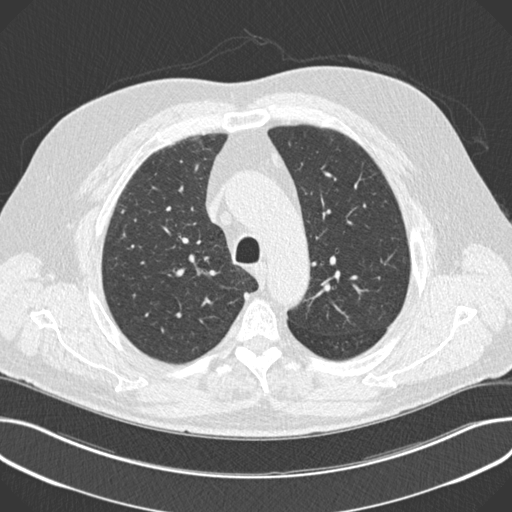
Axial slice from a low-dose chest CT screening exam; first (baseline) screen; lung window (W 1500 / L -600 HU). Male, age 64 years at enrolment. Current smoker at enrolment.
Lesion marked by an expert reader, bounding box (x1, y1, x2, y2) in pixels: (111, 200, 136, 225). No non-calcified nodule or mass ≥4 mm was recorded by the screening reader at this exam. Official screen result: negative screen, no significant abnormalities. Lung cancer was diagnosed 854 days after this screen: squamous cell carcinoma, NOS, right upper lobe, moderately differentiated (G2), stage IA (AJCC 6th edition), 7 mm at pathology.